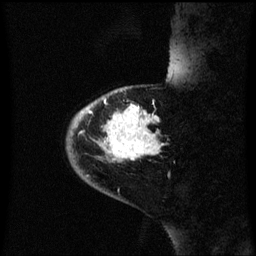
Breast MRI (dynamic contrast-enhanced), one sagittal slice; position 13 of 60 along the scan axis; dynamic contrast-enhanced series, image 2 of 3 at this slice position (ordered by acquisition); 1.5 T; TE 4.2 ms, TR 8.4 ms; 2.3 mm slice thickness; 256 × 256 image matrix. Patient: female, 46 years. From the clinical record (not read from this slice): setting: breast cancer imaged before/during neoadjuvant chemotherapy; receptor status: HER2-positive.
Outlined on this slice (semi-automatically segmented with operator editing):
- analysis volume of interest (the breast-tissue region the enhancement analysis was run in; not a lesion): bounding box (x1, y1, x2, y2) in pixels: (66, 86, 165, 171)
- tumour enhancement mask (voxels above the 70 % enhancement threshold inside the analysis volume of interest): (76, 106, 163, 161)